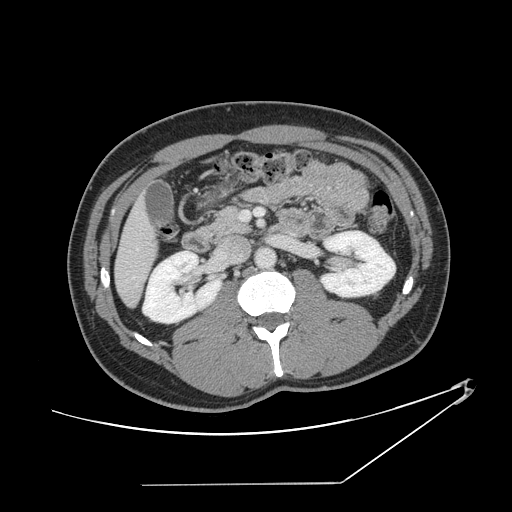
Contrast-enhanced abdominal CT, one axial slice. Reconstruction kernel STANDARD. 120 kVp. Intravenous contrast given. Soft-tissue window (W 400 / L 40 HU). 2.5 mm slice thickness. 512 × 512 image matrix, field of view 432 × 432 mm. Male patient, age 45 years. Case-level facts recorded for this patient, not image findings: diagnosis: colorectal cancer liver metastases, imaged before liver resection; multiple liver metastases: no; largest metastasis: 1 cm.
Outlined on this slice (manually delineated by an expert):
- hepatic veins: bounding box (x1, y1, x2, y2) in pixels: (129, 247, 139, 252)
- liver: (117, 203, 155, 306)
- planned liver remnant (the part of the liver to remain after resection): (117, 202, 155, 306)
- portal vein (with intrahepatic branches): (240, 208, 264, 220)